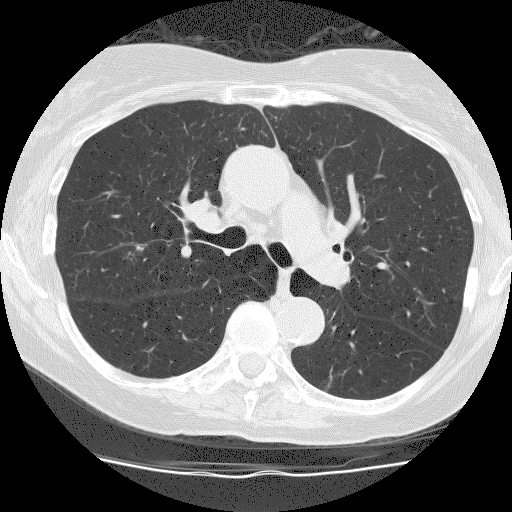
Chest CT (low-dose screening protocol), one axial image, second annual screen, lung window (W 1500 / L -600 HU), lung (sharp) reconstruction kernel (BONE), 512 × 512 image matrix, field of view 300 × 300 mm. Female participant, aged 66 years at enrolment.
- Expert reader's lesion annotation, bounding box <109,231,160,276> (left, top, right, bottom; pixels).
- The screening reader recorded 2 non-calcified nodules or masses ≥4 mm on this exam (right upper lobe, right lower lobe); which of them this box marks is not recorded.
- Lung cancer was diagnosed 209 days after this screen: squamous cell carcinoma, NOS, right upper lobe, stage IIIA (AJCC 6th edition), 10 mm at pathology.